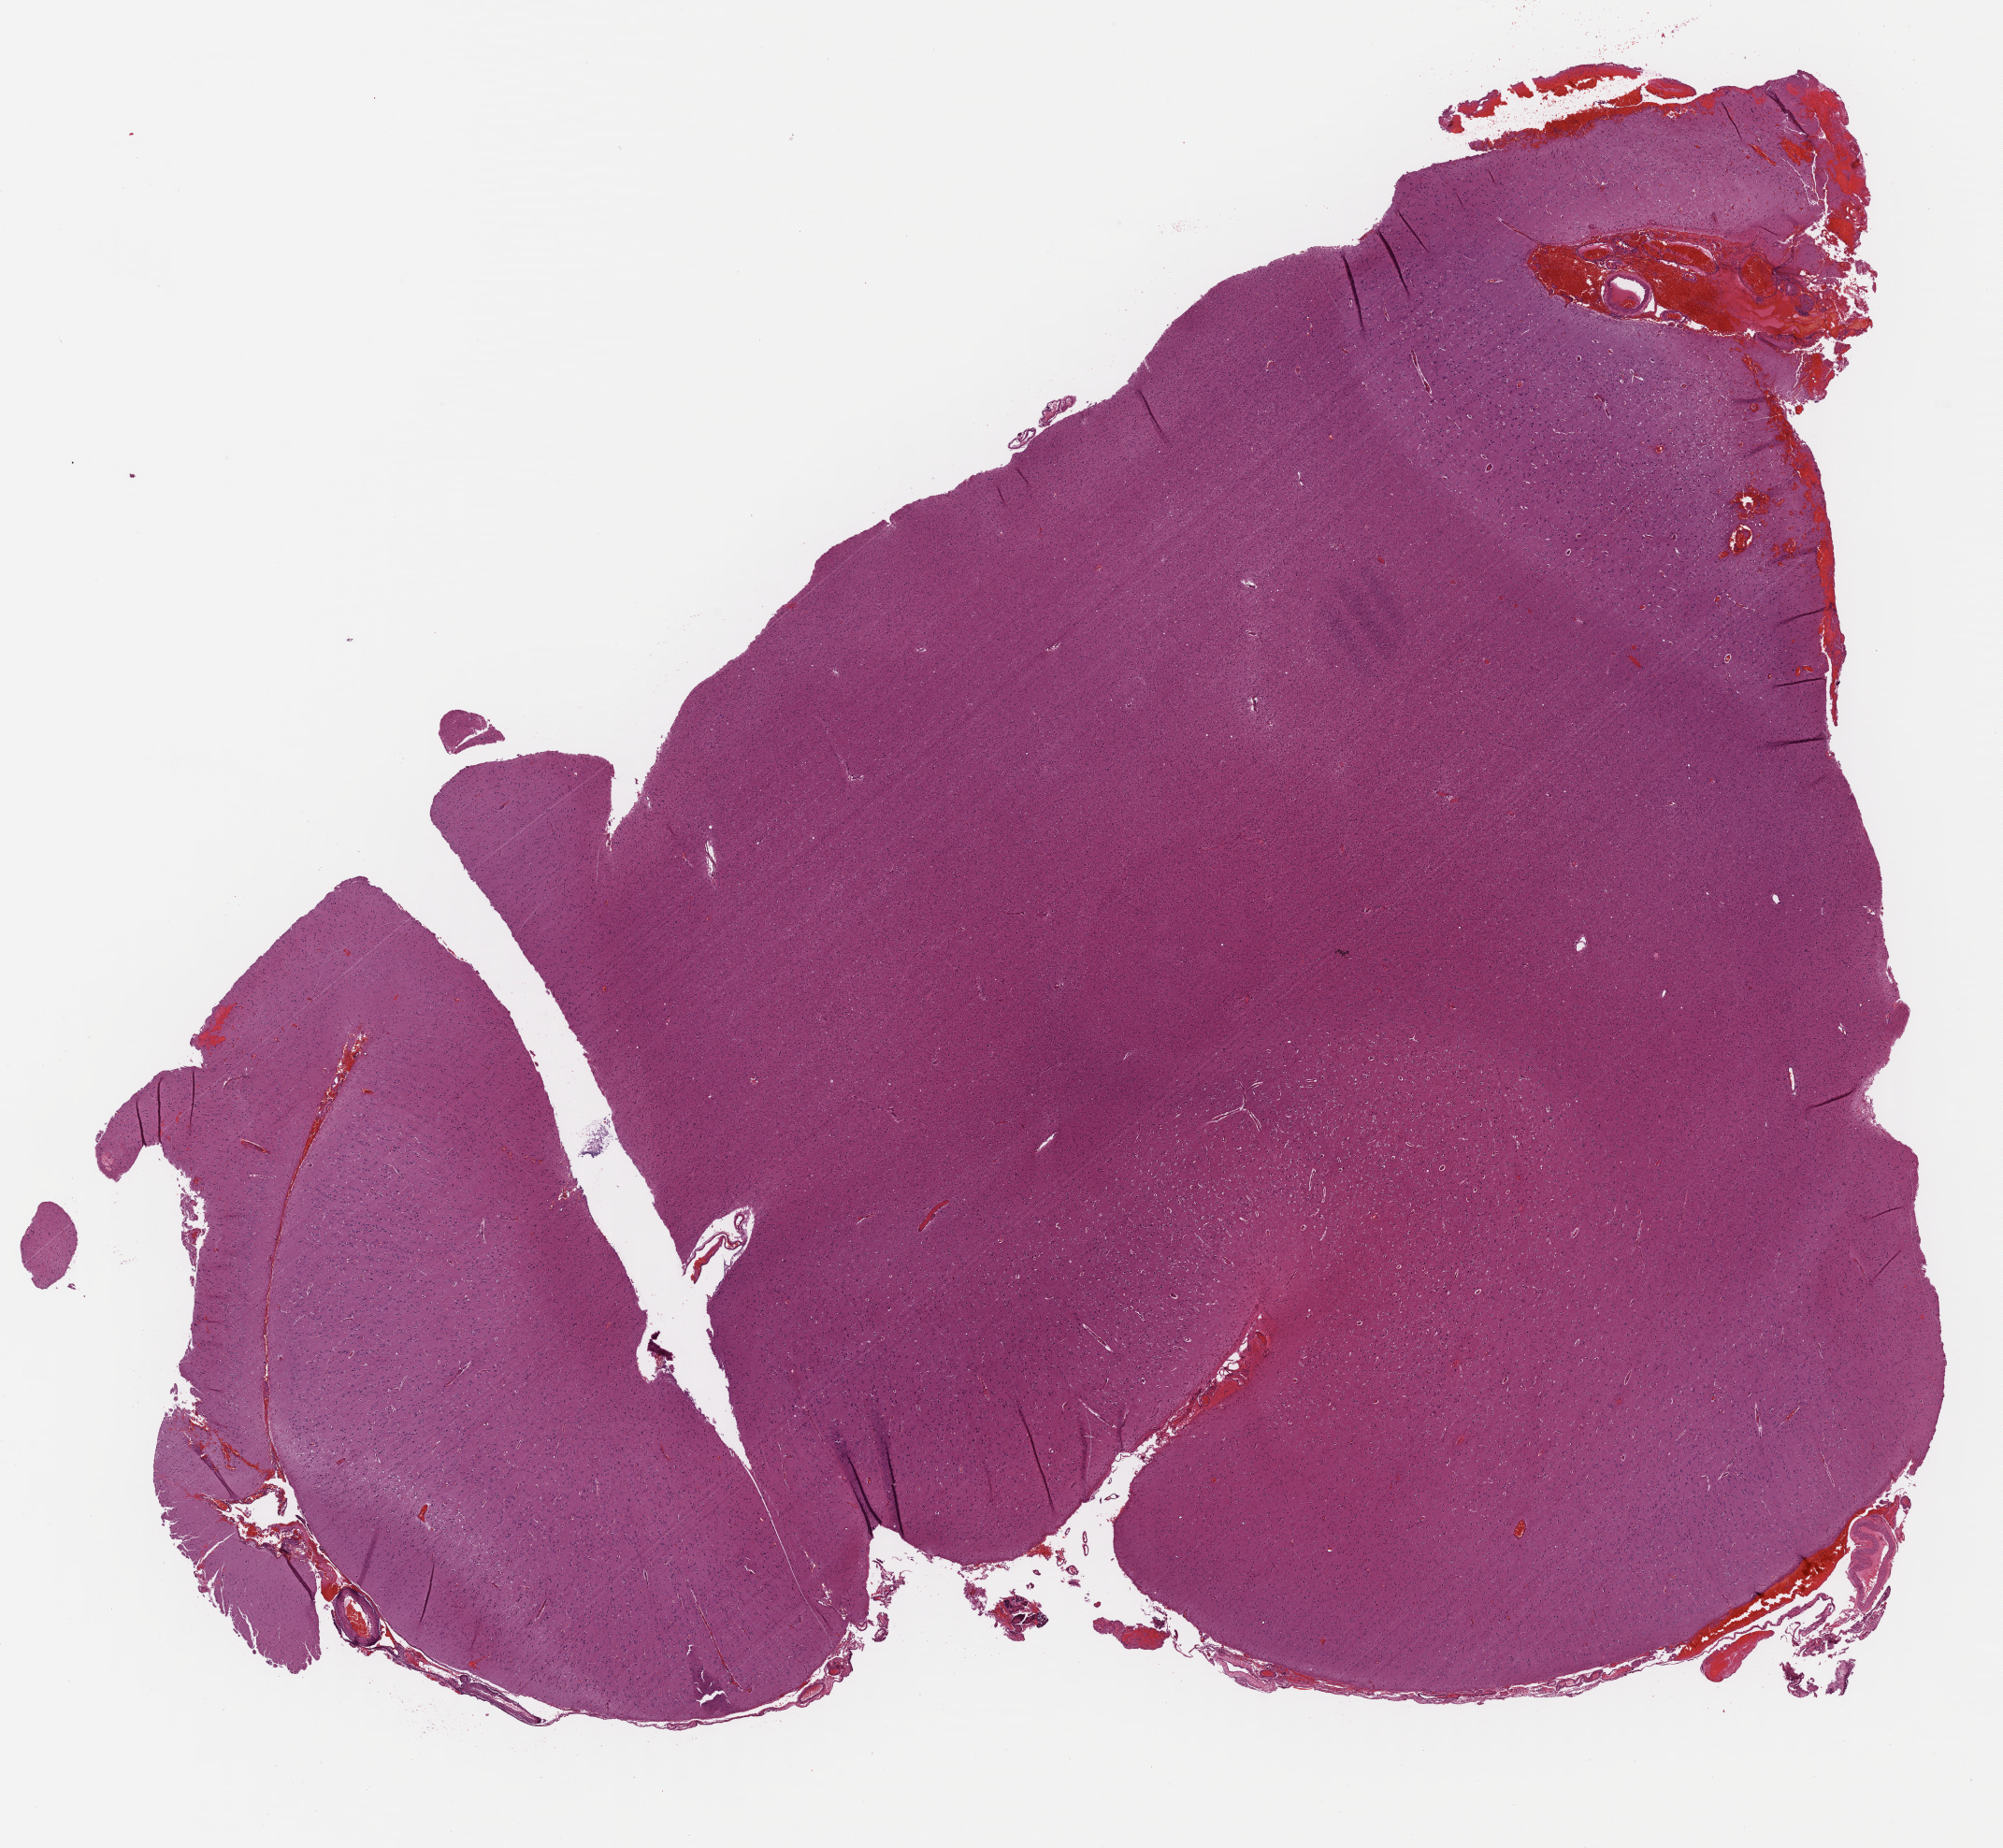
H&E-stained whole-slide image — shown as a low-resolution overview of the whole scanned area (about 16.8 x 15.5 mm), formalin-fixed paraffin-embedded (FFPE) diagnostic section, sample: primary tumour, brain. Female patient; age at initial diagnosis 61 years. Histologic grade: G2 (moderately differentiated).
Laterality: left. Histologic diagnosis: Astrocytoma, NOS (cerebrum).